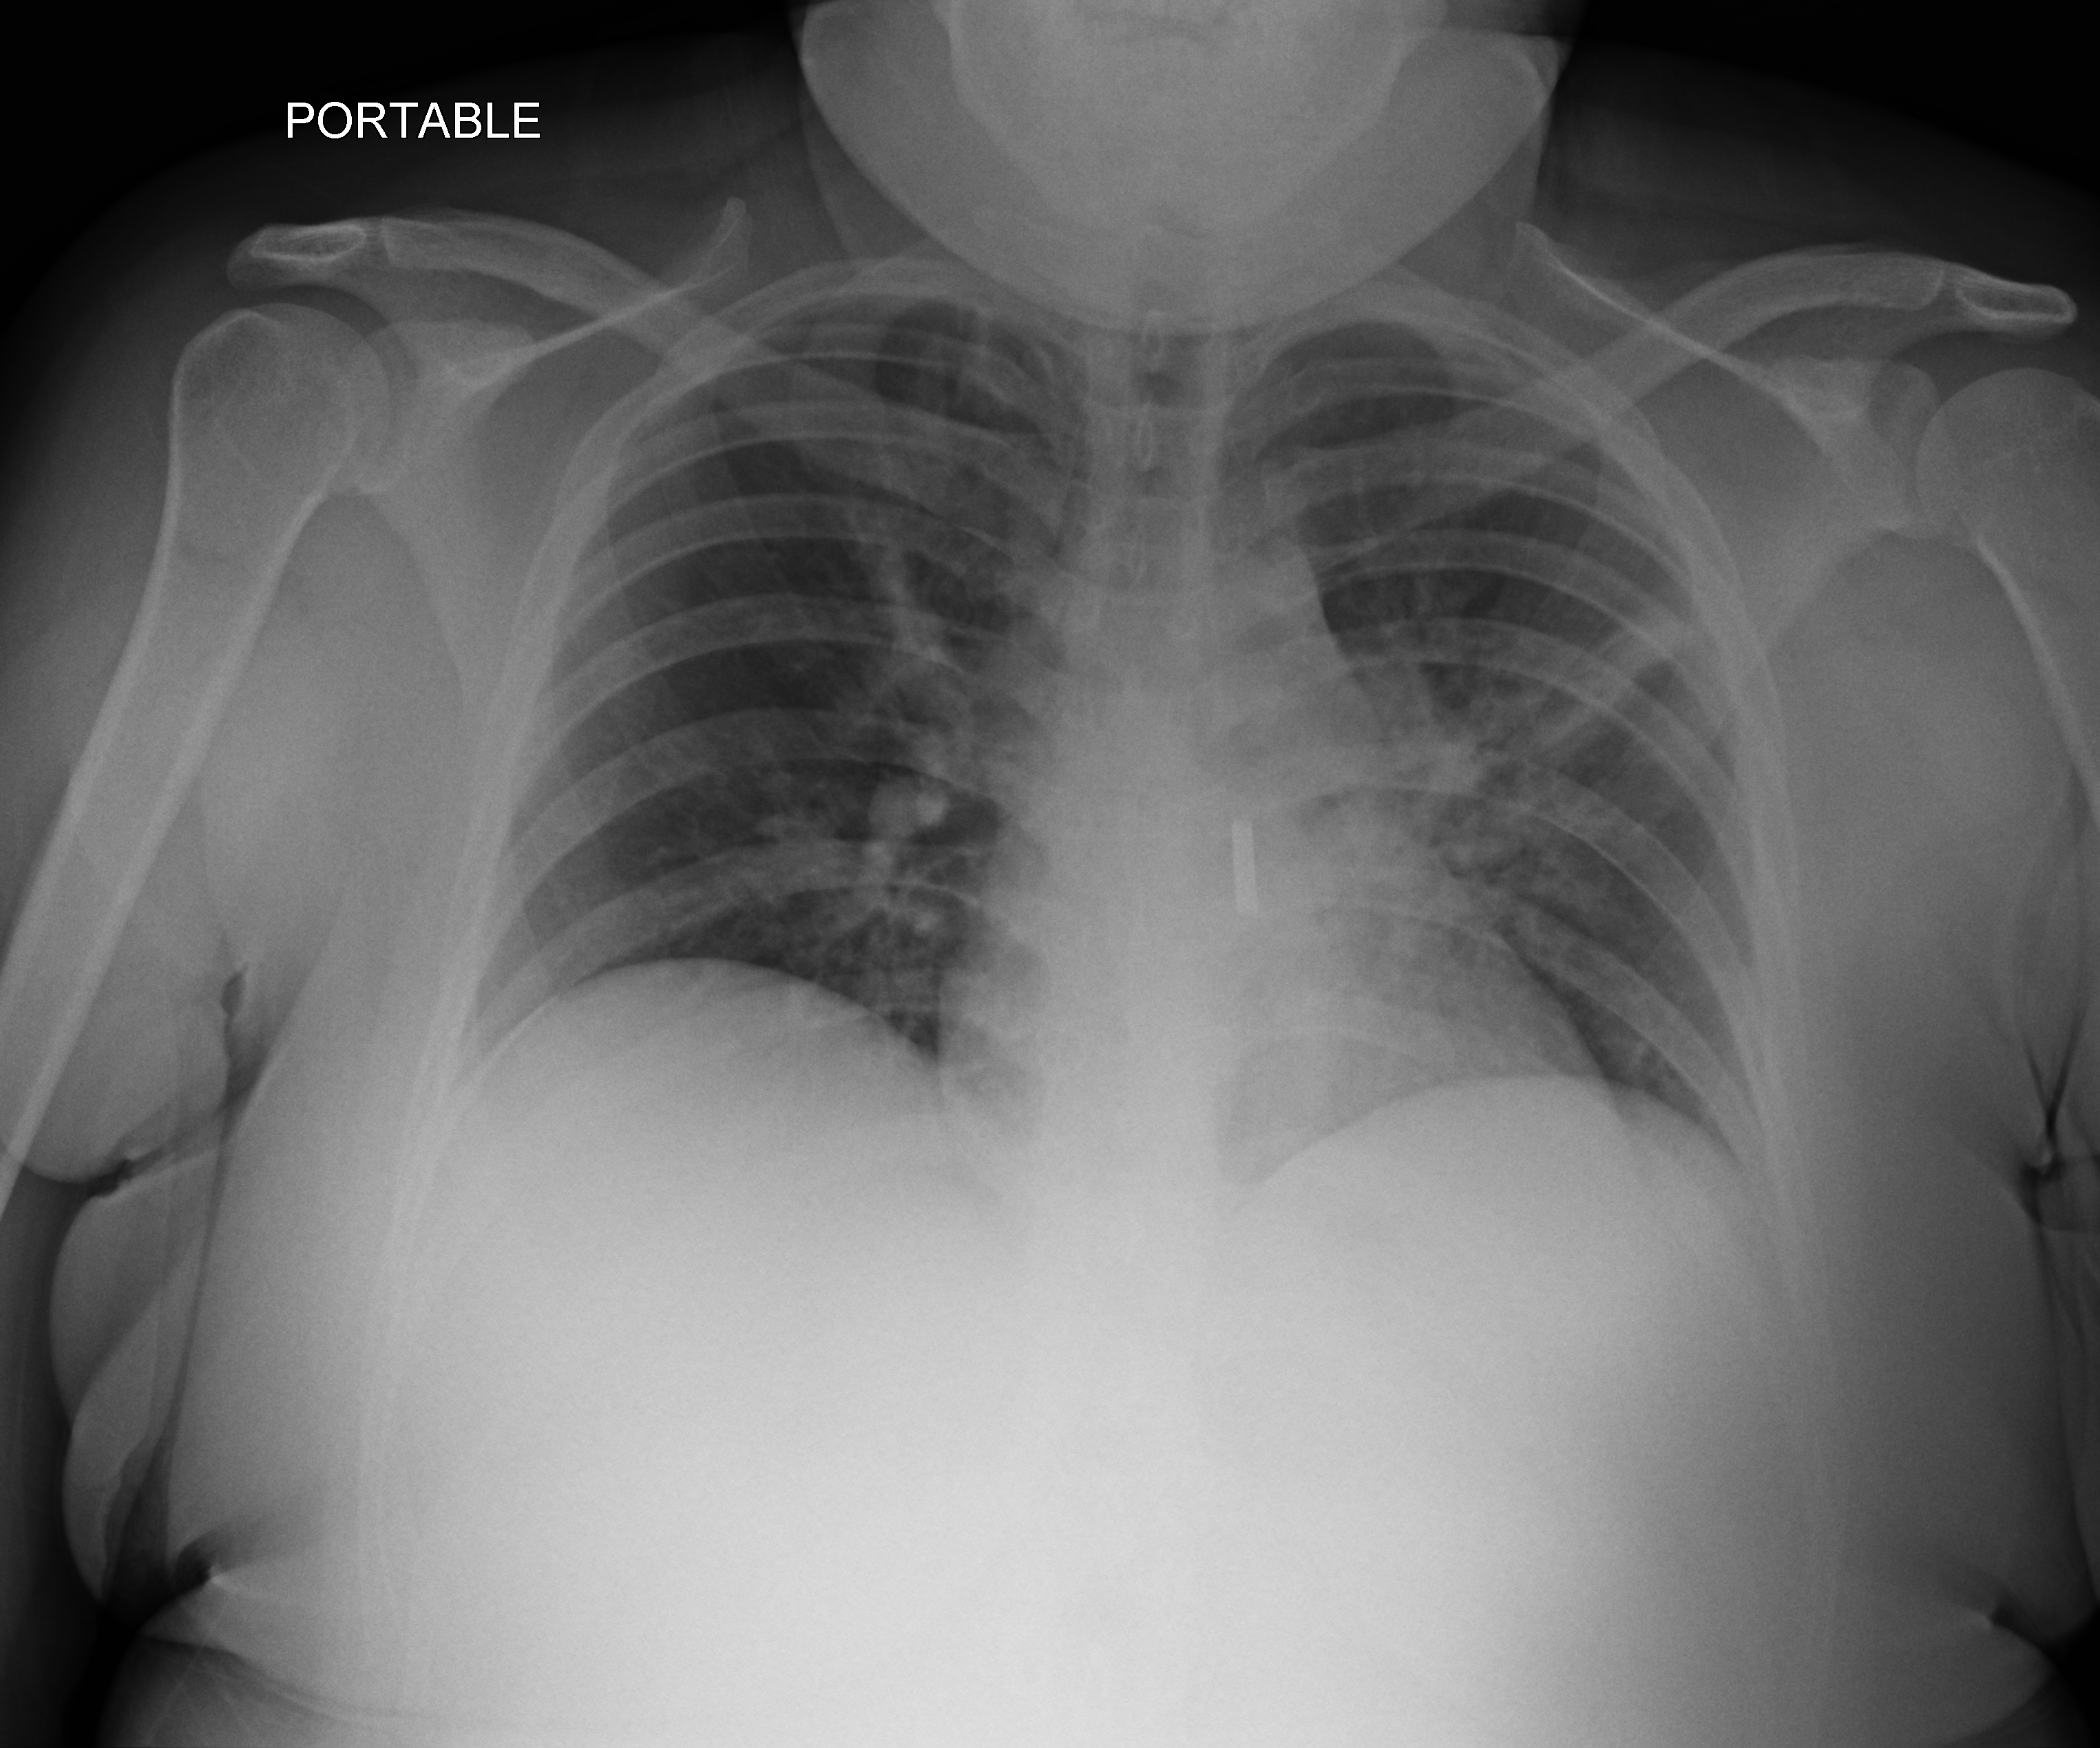
Bedside chest radiograph (computed radiography). Patient hospitalised with COVID-19; female, aged 18–59 years.
From the hospital-stay record, not from the radiograph (when in the stay this image was taken is not recorded):
- hypertension (admission record): no
- mechanically ventilated during this hospital stay: no